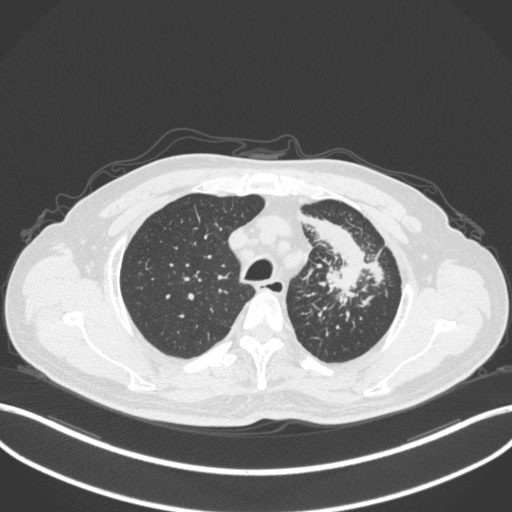
Chest CT, one axial slice. Slice 284 of 386 in the series (ordered by position). 120 kVp. Lung window (W 1500 / L -600 HU). 1 mm slice thickness. 512 × 512 image matrix, field of view 400 × 400 mm. Male patient, age 69 years. From the clinical record (not read from this slice): clinical TNM (as recorded): T2a N2 M0.
Outlined on this slice (bounding box drawn by a radiologist):
- lung tumour (recorded histology: adenocarcinoma): box from (x=301, y=211) to (x=387, y=299) px